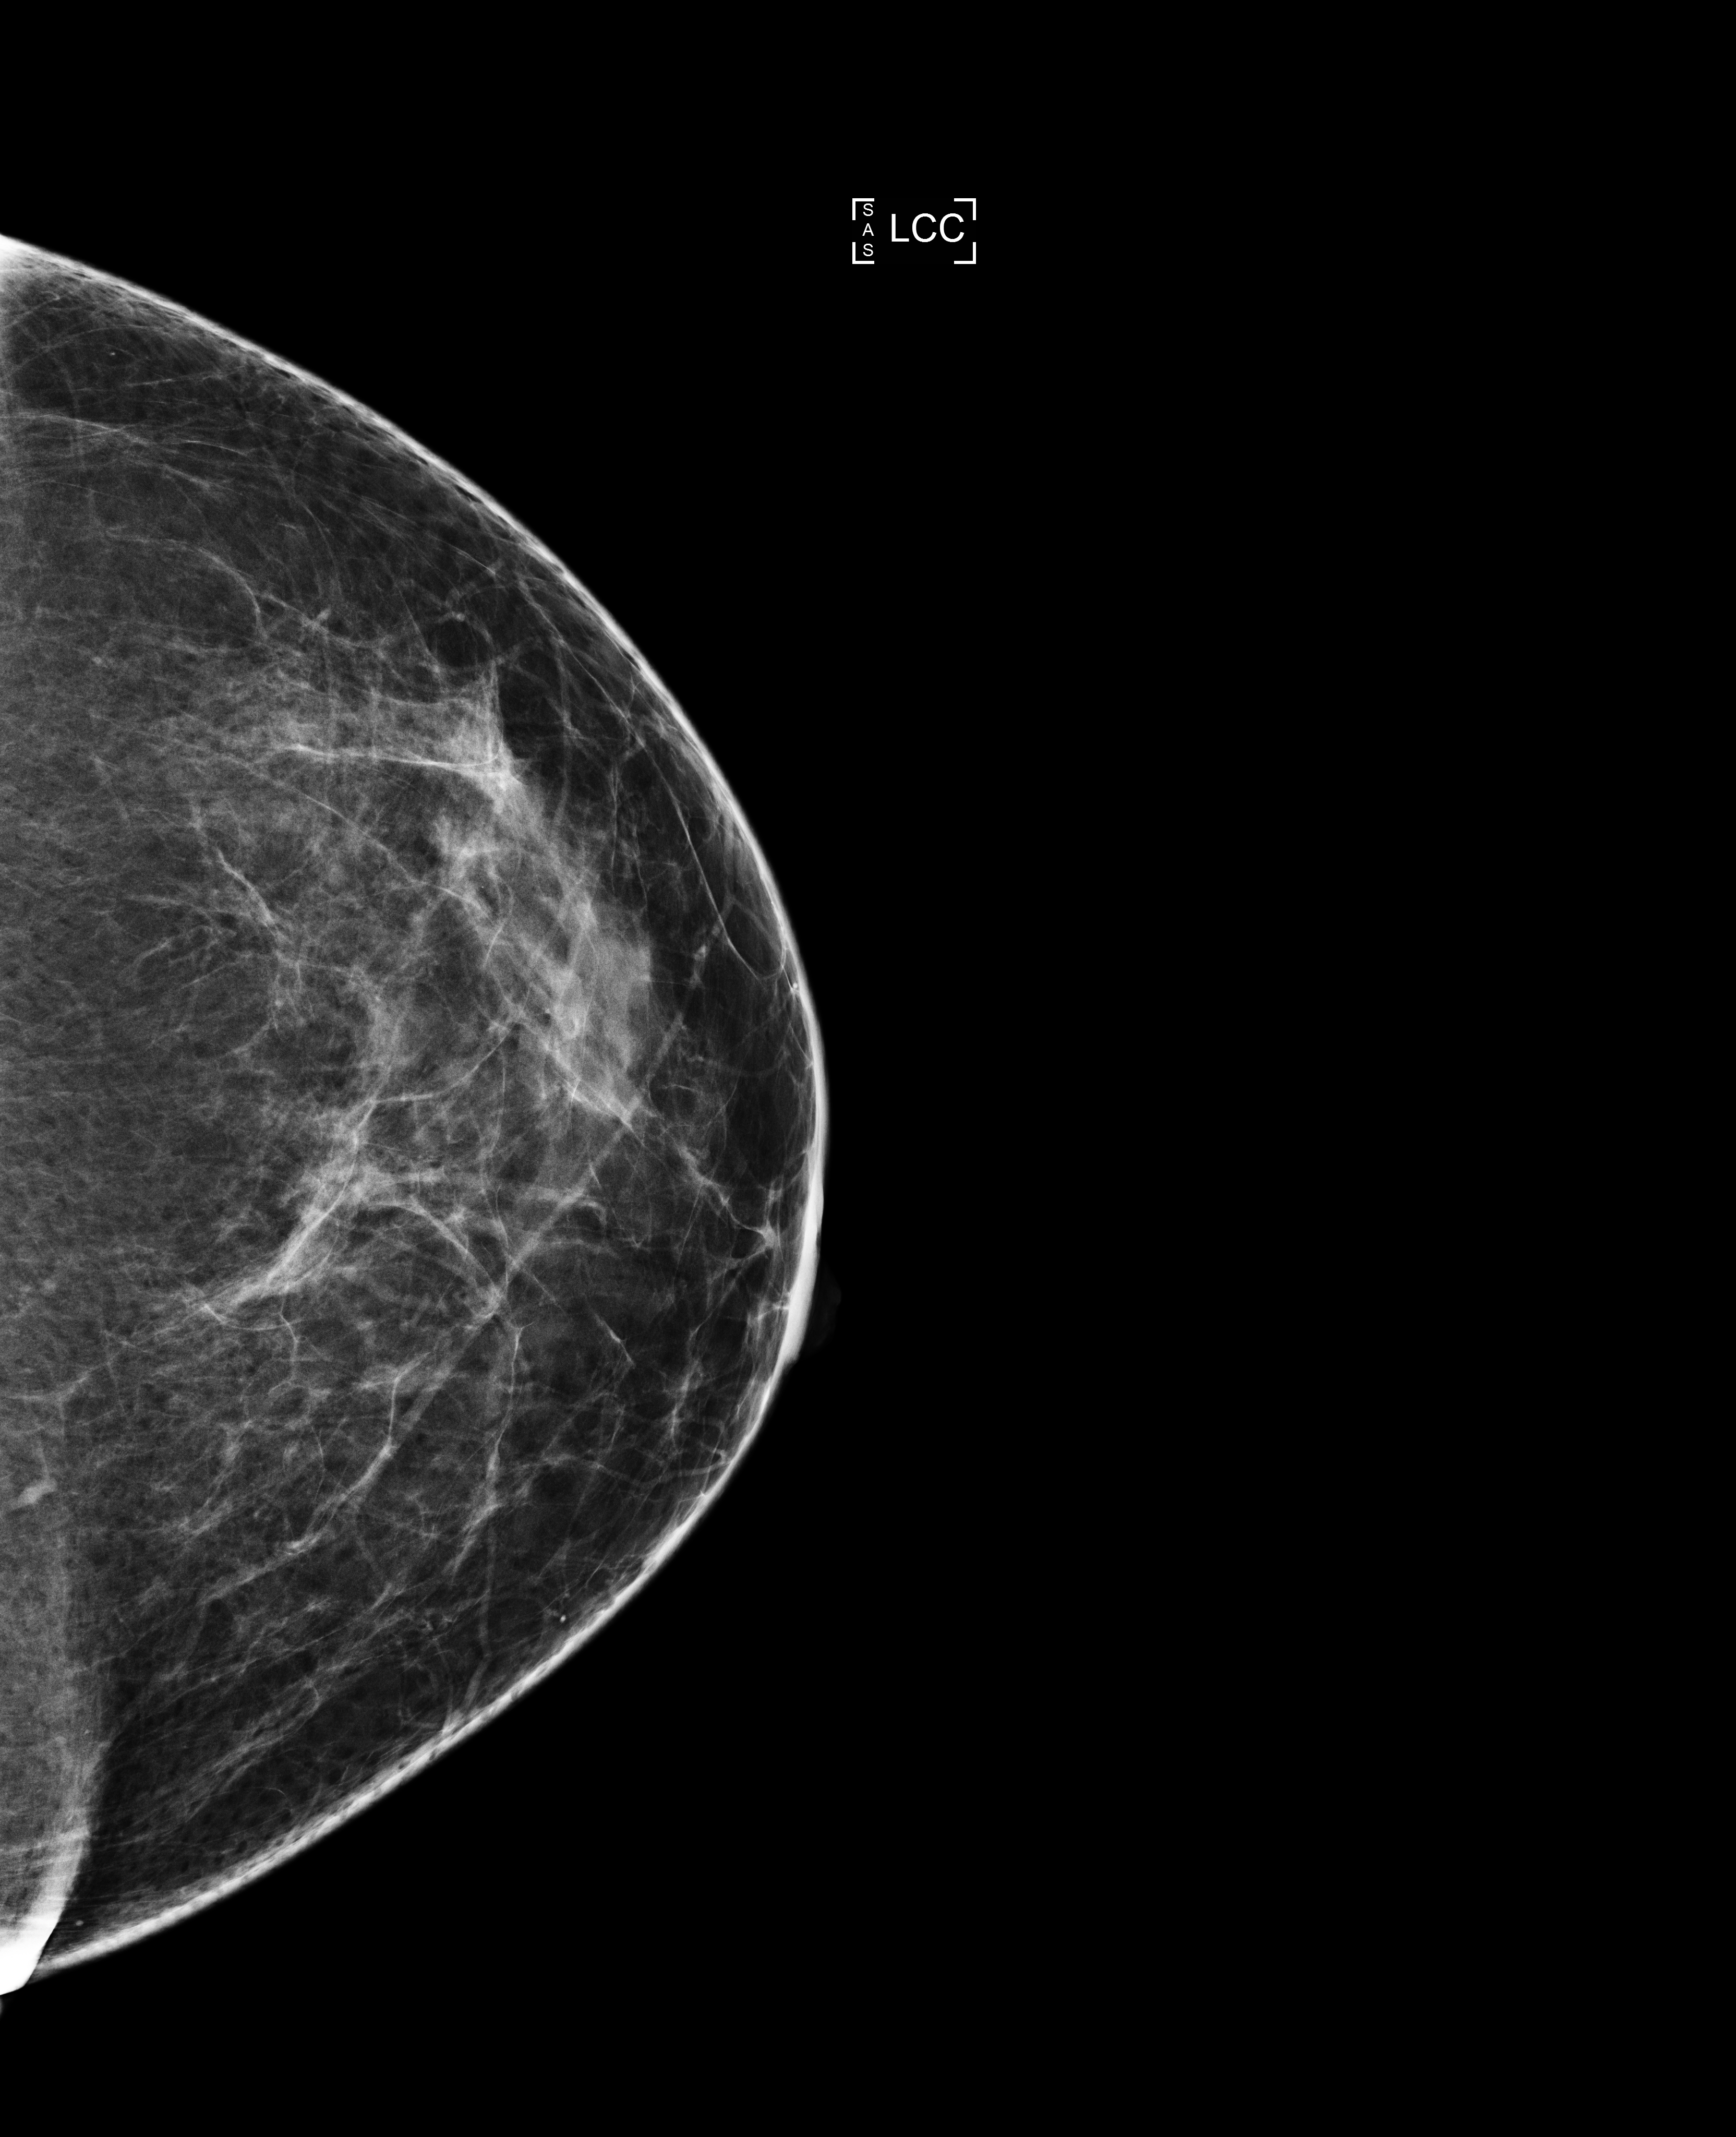
Digital mammogram (FFDM), left breast, craniocaudal (CC) view, screening examination, compressed breast thickness 59 mm, system: Selenia Dimensions. Patient aged 46 years (female).
- BI-RADS breast density category at the screening exam (both breasts, scale 1–4): 3
- final BI-RADS category for the screening round (tomosynthesis exam, both breasts): category 1
- recall: no recall after this screen